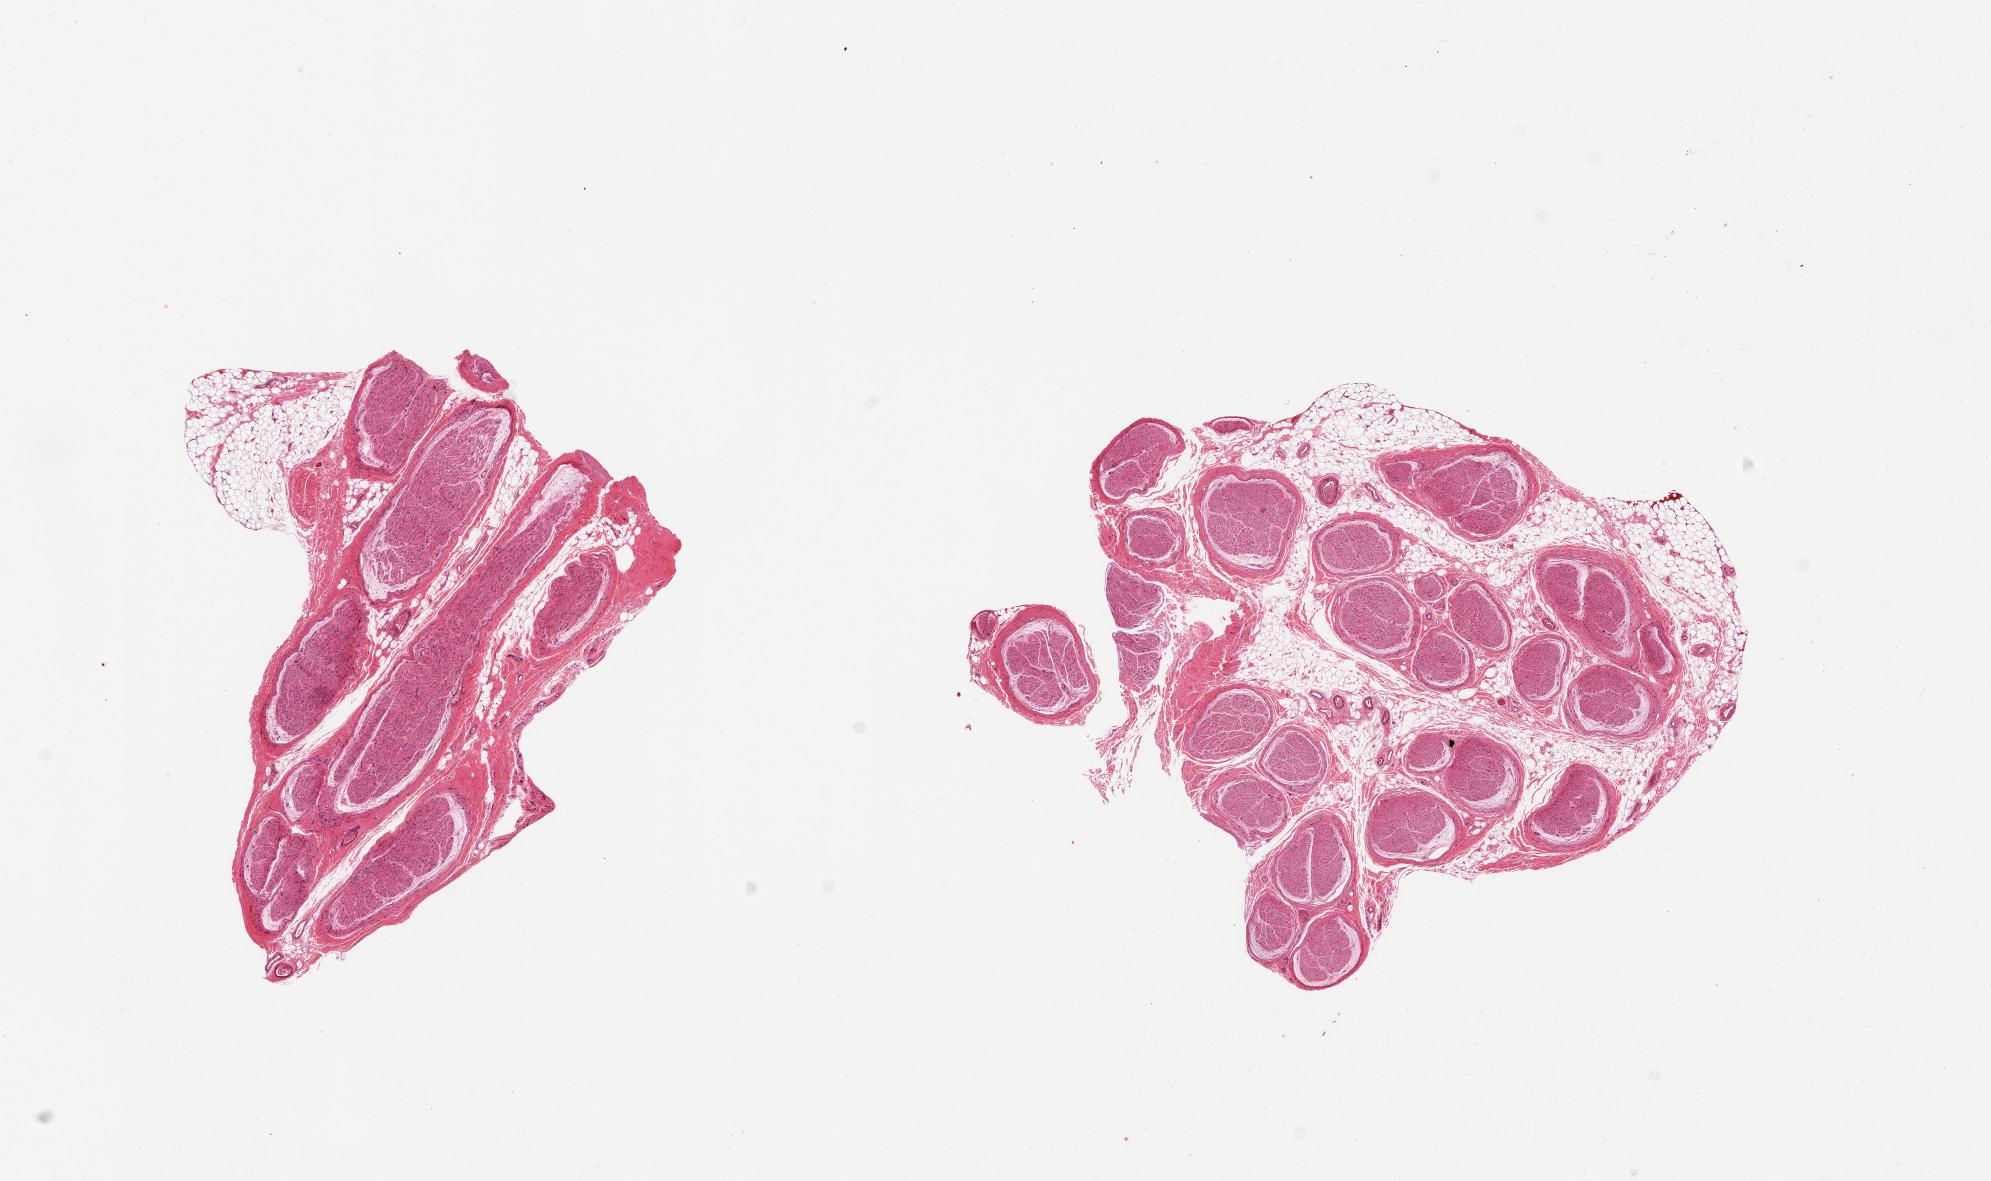
Whole-slide image, H&E stain, brightfield, shown as a low-resolution overview of the whole scanned area (about 15.8 x 9.3 mm, acquisition: 20x scan); PAXgene-fixed, paraffin-embedded tissue; target tissue: tibial nerve; donor tissue sample. Donor sex: female.
• review note (as recorded): 2 pieces; up to 30% internal and external fat